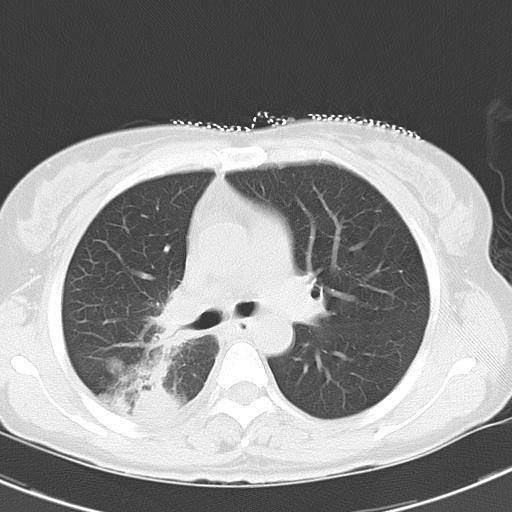
Chest CT, one axial slice; reconstruction kernel B70f; 120 kVp; lung window (W 1500 / L -600 HU); 512 × 512 image matrix, field of view 300 × 300 mm. Female patient, age 47 years. From the clinical record (not read from this slice): clinical TNM (as recorded): T1c N3 M0.
Outlined on this slice (bounding box drawn by a radiologist):
- lung tumour (recorded histology: adenocarcinoma): bounding box <93,345,183,418> (left, top, right, bottom; pixels)